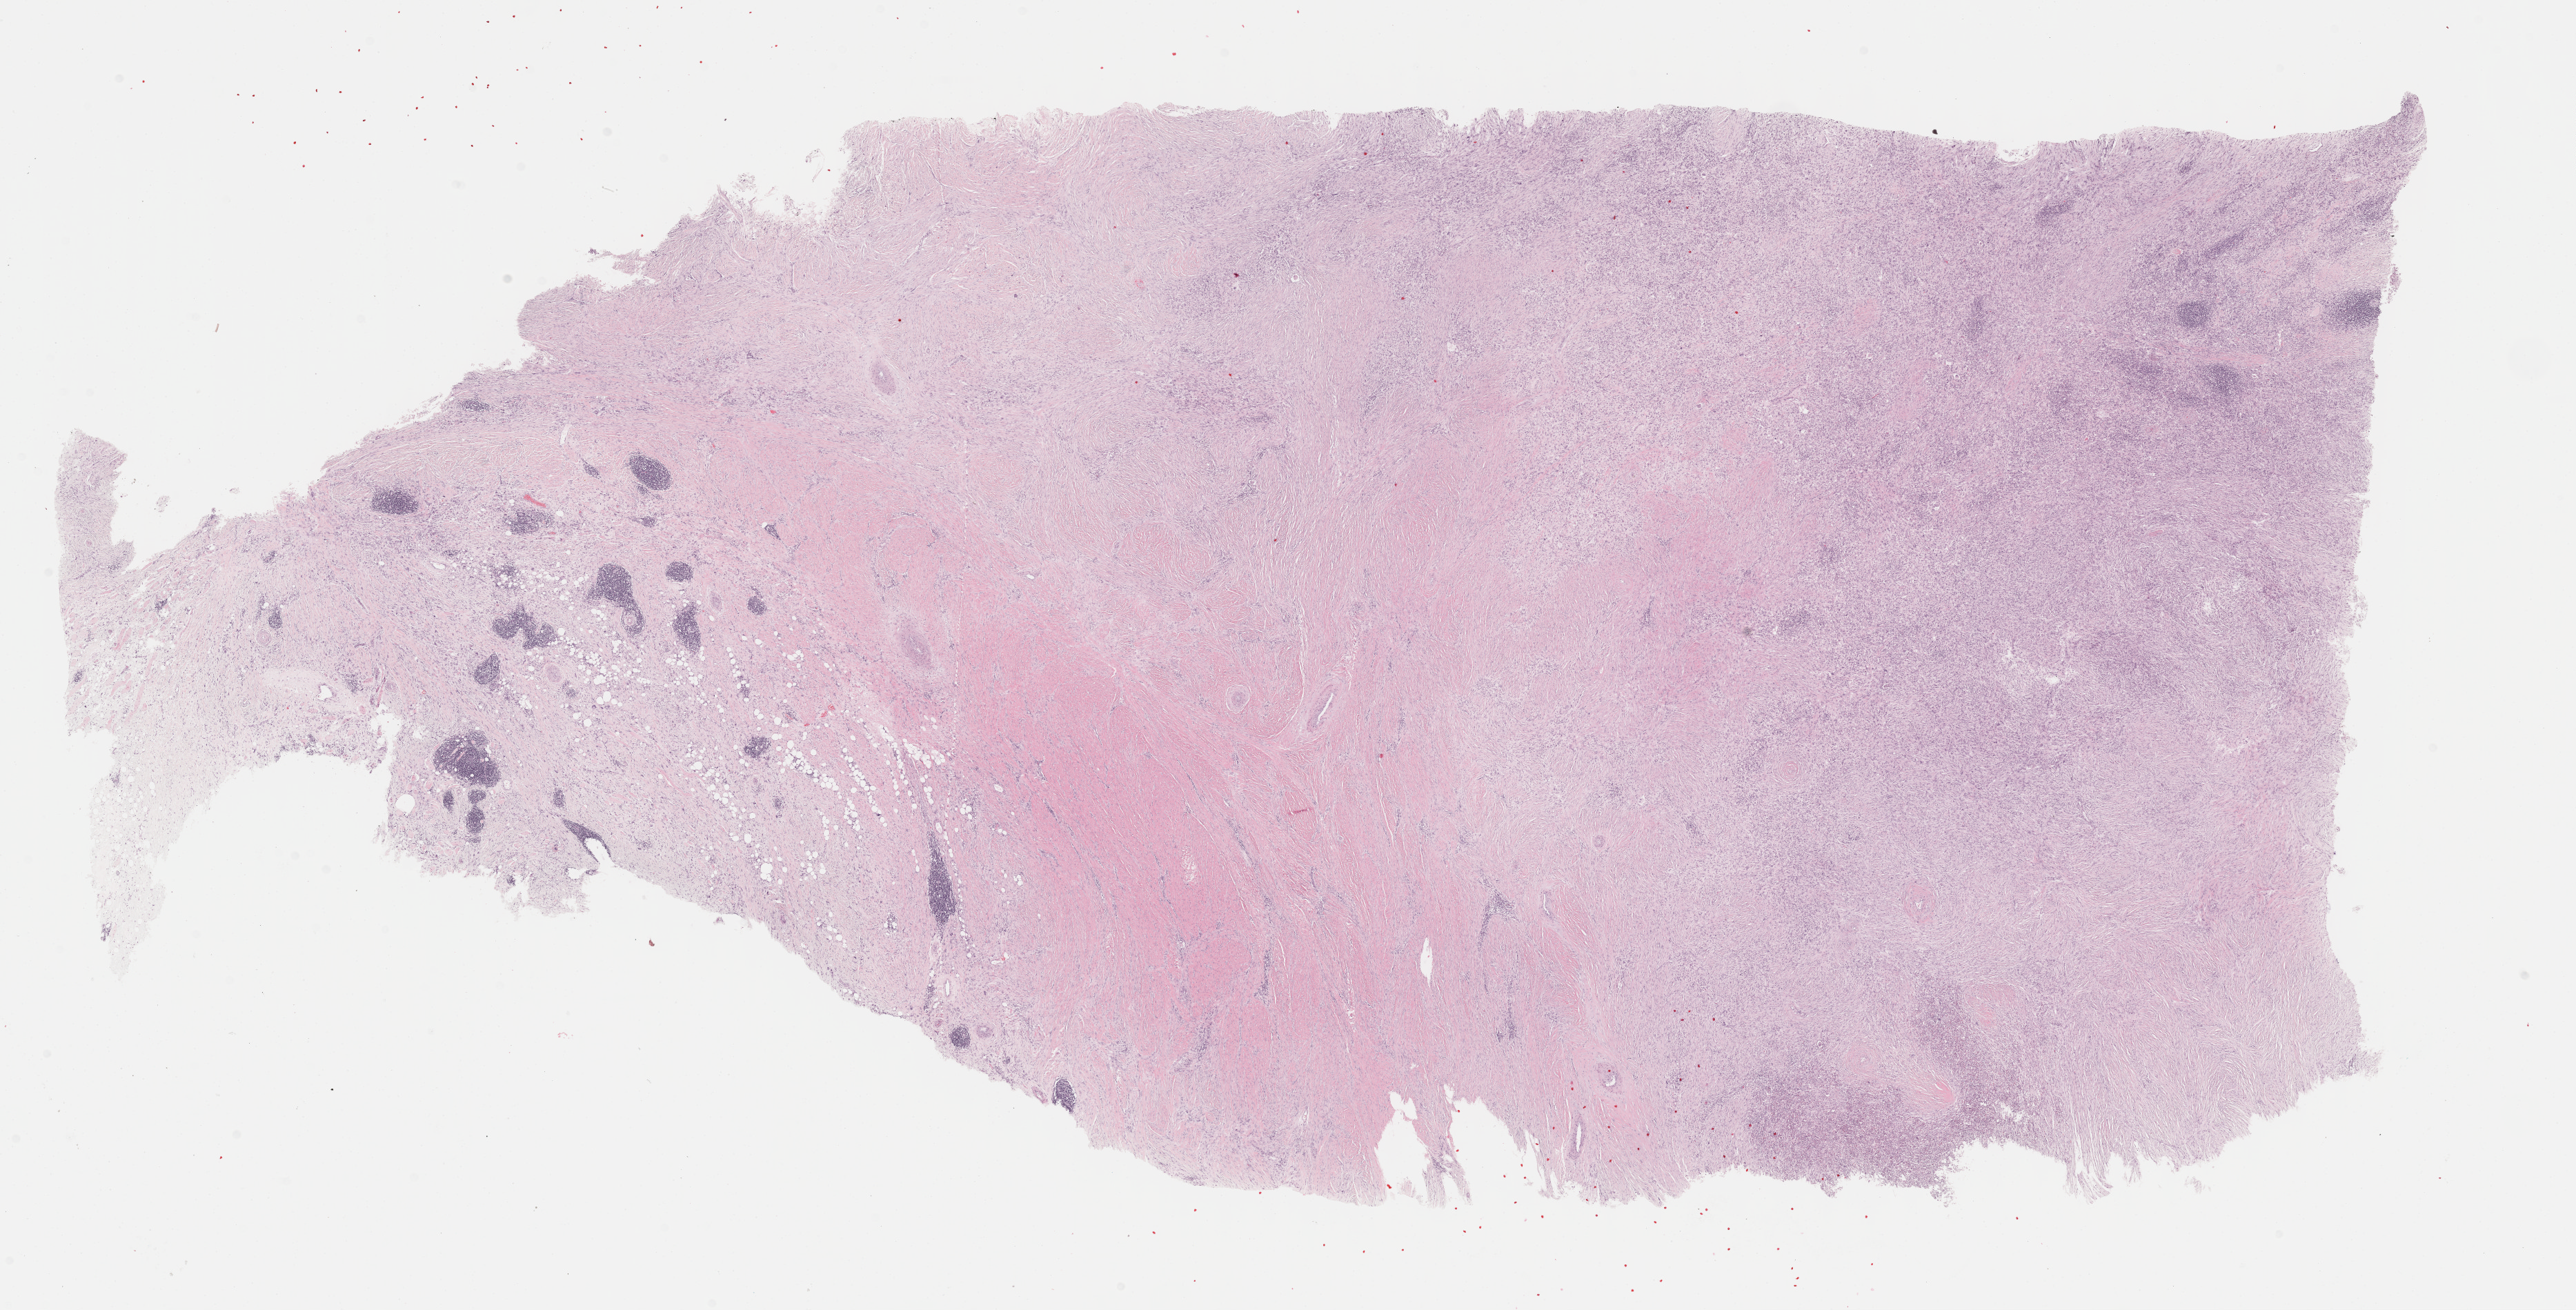
Digitized Hematoxylin and eosin (H&E) stained tissue section (whole slide) — a low-resolution overview of the entire scanned area, about 30.2 x 15.4 mm, formalin-fixed paraffin-embedded (FFPE) diagnostic section, sample: primary tumour, retroperitoneum and peritoneum. Patient: male, age at initial diagnosis 60 years.
Histologic diagnosis: Dedifferentiated liposarcoma (retroperitoneum).